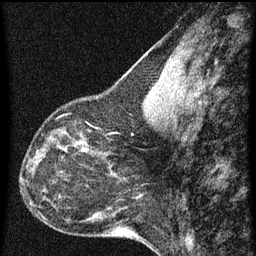
Breast MRI (dynamic contrast-enhanced), one sagittal slice; slice 26 of 60 in the series (ordered by position); dynamic contrast-enhanced series, image 2 of 3 at this slice position (ordered by acquisition); 1.5 T; TE 4.2 ms, TR 8 ms; 256 × 256 image matrix, field of view 180 × 180 mm. Female patient, age 44 years.
Structures marked on this image (semi-automatic segmentation, software-assisted and operator-edited):
- analysis volume of interest (the breast-tissue region the enhancement analysis was run in; not a lesion): box from (x=49, y=128) to (x=95, y=169) px
- tumour enhancement mask (voxels above the 70 % enhancement threshold inside the analysis volume of interest): (x=49, y=130)–(x=61, y=149)